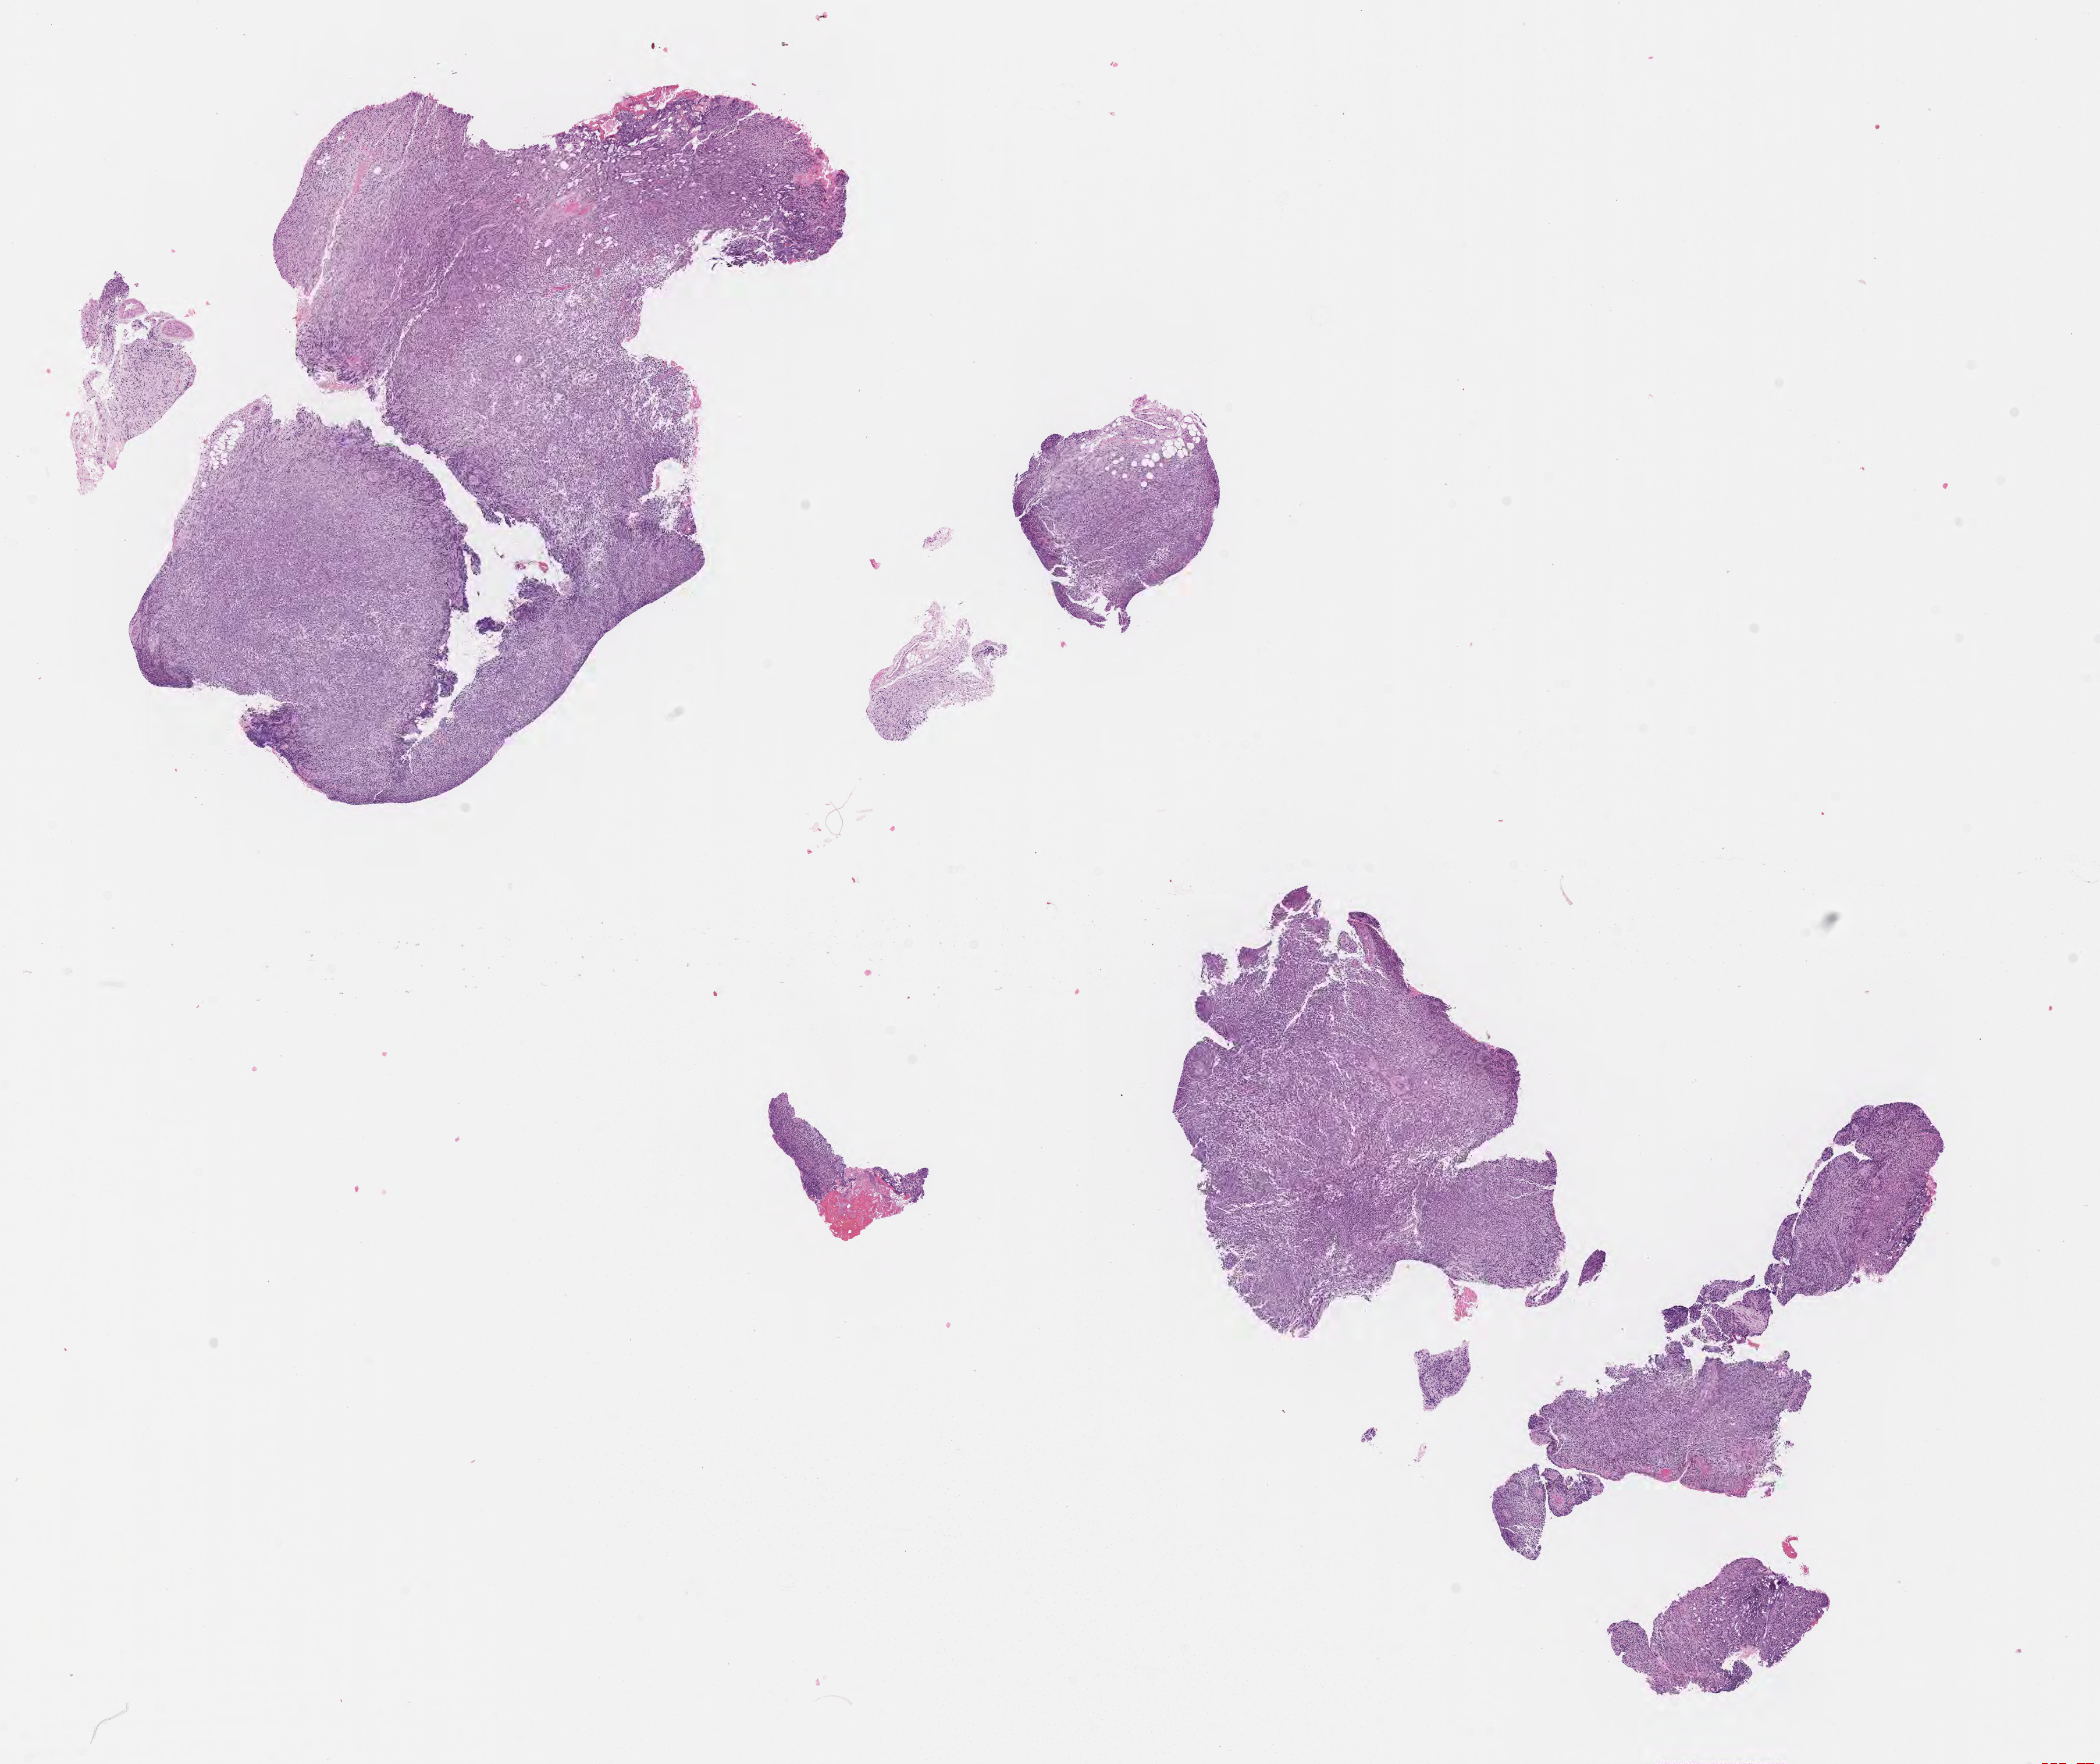
Digitized H&E-stained section of tumor tissue, a low-resolution overview of the entire scanned area, about 14.6 x 12.3 mm, formalin-fixed paraffin-embedded section, sample anatomic site: orbit, right. Patient: female, age 6.3 years at diagnosis.
- metastatic status at presentation (as recorded): non-metastatic
- diagnosis: rhabdomyosarcoma; histological classification: spindle cell rhabdomyosarcoma
- stage (as recorded): 1